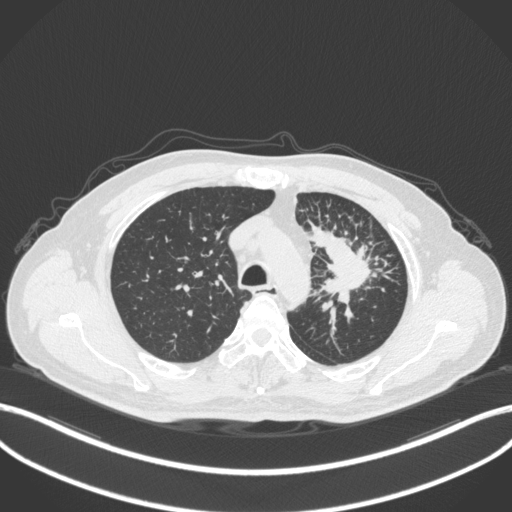
Chest CT, one axial slice; slice 269 of 386 in the series (ordered by position); 120 kVp; lung window (W 1500 / L -600 HU); 512 × 512 image matrix, field of view 400 × 400 mm. Patient: male, 69 years. From the clinical record (not read from this slice): clinical TNM (as recorded): T2a N2 M0; histopathological grade: G2-3.
Outlined on this slice (bounding box drawn by a radiologist):
- lung tumour (recorded histology: adenocarcinoma): bounding box <312,225,371,305> (left, top, right, bottom; pixels)